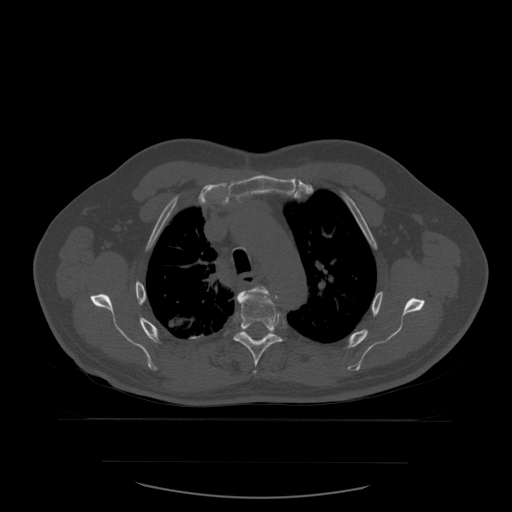
CT including the spine, one axial slice. Position 425 of 590 along the scan axis. Bone window (W 1800 / L 400 HU). 1.25 mm slice thickness. 512 × 512 image matrix, field of view 479 × 479 mm. Patient age 71 years. Case-level facts recorded for this patient, not image findings: primary cancer: lung.
Outlined on this slice (semi-automatically segmented with operator editing):
- T4 vertebra: bounding box [x1, y1, x2, y2] px = [244, 286, 269, 373]
- T5 vertebra: [234, 292, 283, 367]
- T6 vertebra: [251, 333, 271, 341]